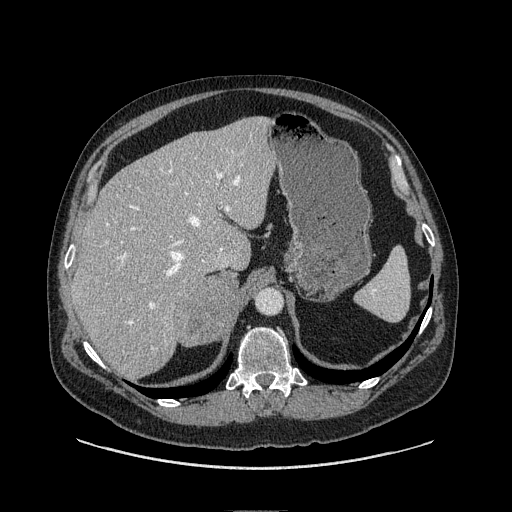
Contrast-enhanced abdominal CT, one axial slice. Position 75 of 149 along the scan axis. Soft-tissue window (W 400 / L 40 HU). 512 × 512 image matrix. Male patient. From the clinical record (not read from this slice): diagnosis: adrenocortical carcinoma; tumour side: right adrenal; tumour size at pathology: 7.5 cm; Ki-67 index: 15 %.
Annotated regions visible in this slice (semi-automatically segmented with operator editing):
- mass: bounding box [x1, y1, x2, y2] px = [176, 273, 273, 345]